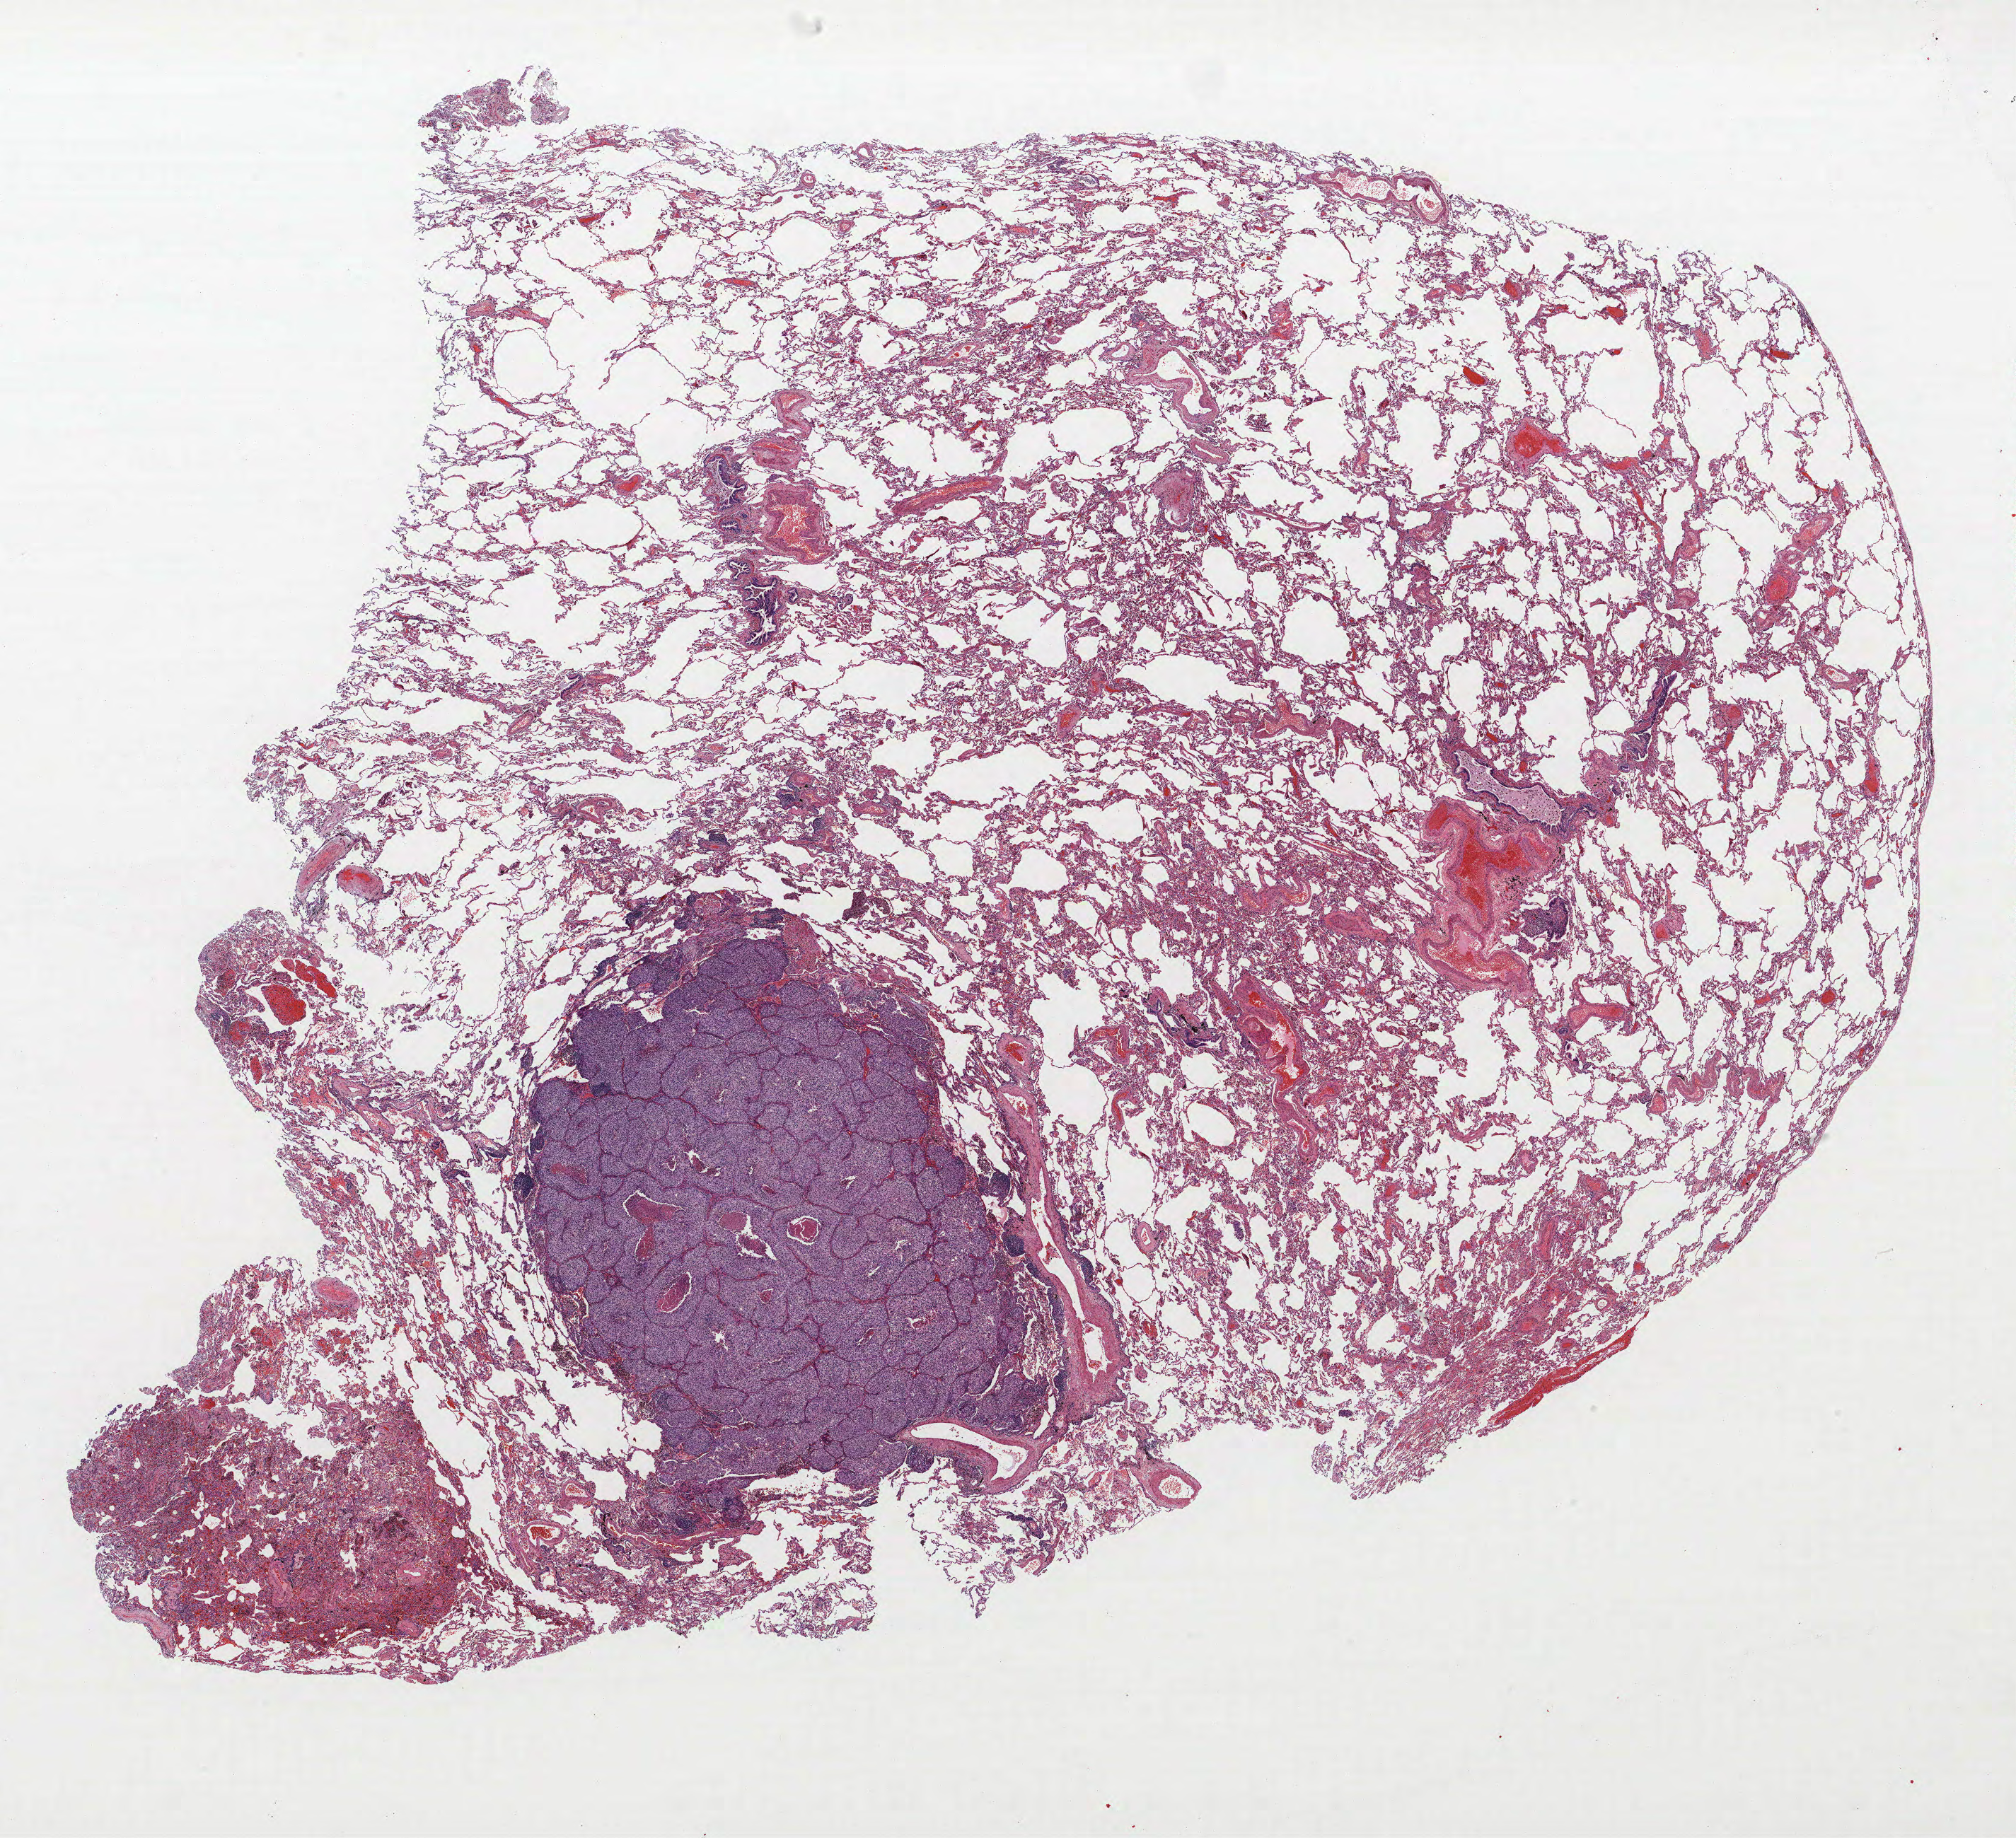
Whole-slide histology image, Hematoxylin and eosin (H&E) stained — whole scanned area (about 22.8 x 20.8 mm, slide scanned at 40x) shown as a low-resolution overview; FFPE section; lung tissue. Female patient, aged 59 at enrolment. Grade: poorly differentiated (G3).
- primary tumour location (clinical record): right lower lobe
- stage (AJCC 6th edition): IA
- tumour size (pathology): 15 mm
- participant's lung-cancer diagnosis: Non-small cell carcinoma